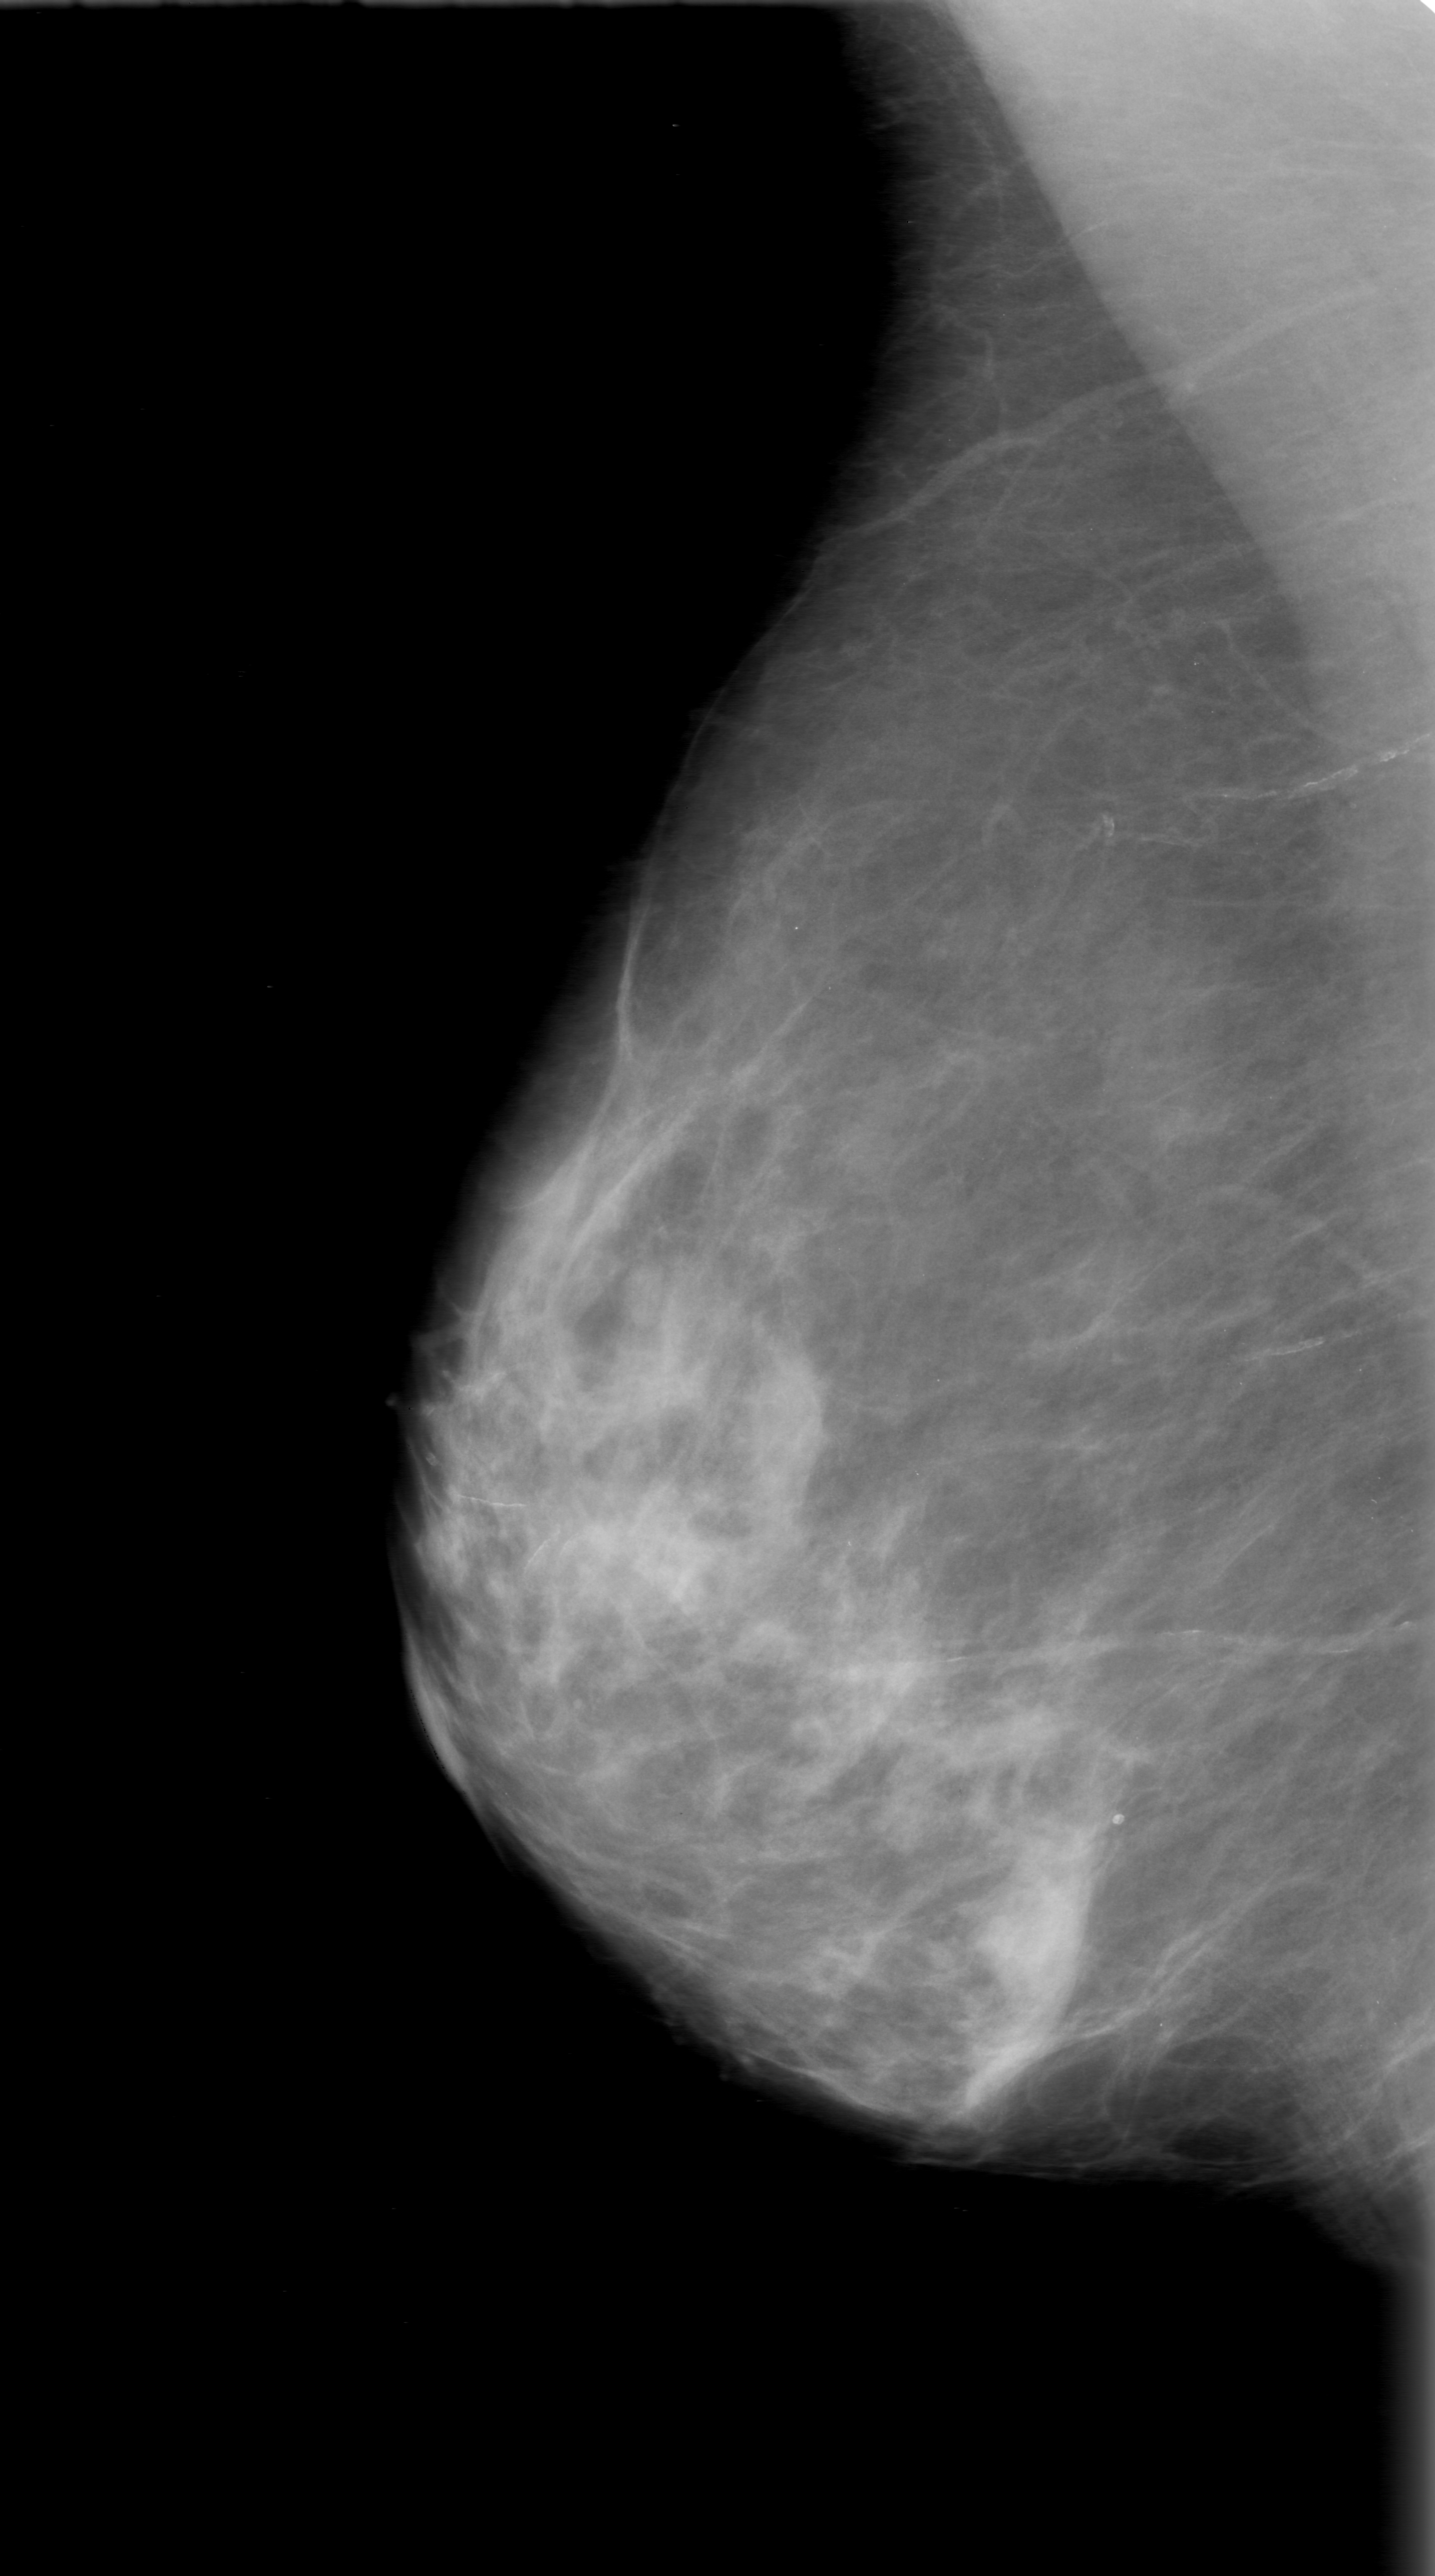
Digitized screen-film mammogram; right breast; mediolateral oblique (MLO) view; 1435 × 2576 image matrix.
Expert-marked regions of interest on this image (one box per marked abnormality):
- mass, shape oval, margins obscured; BI-RADS assessment category 0 (incomplete: needs additional imaging); pathology (as recorded): benign: box from (x=953, y=1844) to (x=1110, y=2031) px